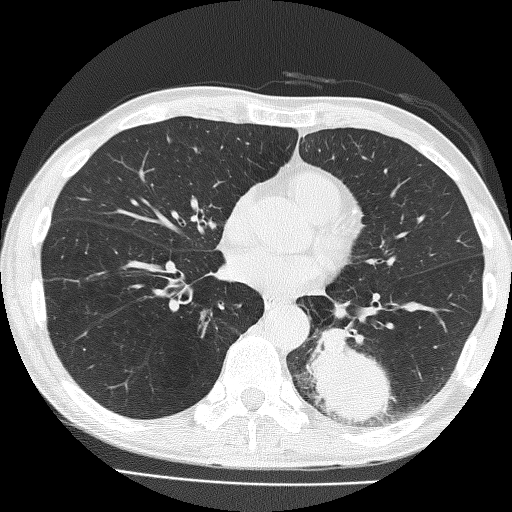
Low-dose screening chest CT, one axial slice; position 74 of 160 along the scan axis; reconstruction kernel FC51; lung window (W 1500 / L -600 HU); 2 mm slice thickness; 512 × 512 image matrix, field of view 324 × 324 mm.
Structures marked on this image (outlined manually by an expert reader):
- lesion 1 (tumor, lower lobe of left lung): bounding box [x1, y1, x2, y2] px = [306, 328, 392, 424]